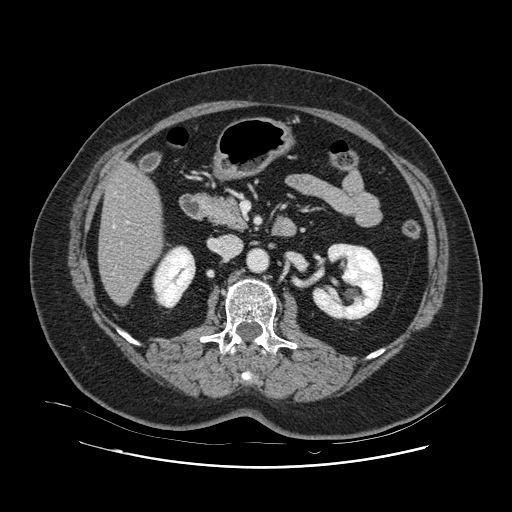
Contrast-enhanced abdominal CT, one axial slice. Slice 36 of 132 in the series (ordered by position). 120 kVp. Soft-tissue window (W 400 / L 40 HU). 2.5 mm slice thickness. 512 × 512 image matrix, field of view 391 × 391 mm. Female patient, age 73 years. Case-level facts recorded for this patient, not image findings: diagnosis: colorectal cancer liver metastases, imaged before liver resection; multiple liver metastases: no; largest metastasis: 7 cm.
Outlined on this slice (expert manual segmentation):
- hepatic veins: bounding box <113,225,115,228> (left, top, right, bottom; pixels)
- liver: <99,165,161,304>
- planned liver remnant (the part of the liver to remain after resection): <99,165,161,304>
- portal vein (with intrahepatic branches): <126,221,129,224>